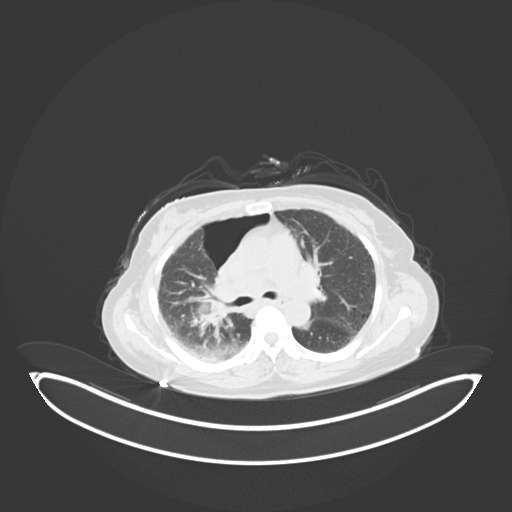
Chest CT, one axial slice; position 35 of 69 along the scan axis; lung window (W 1500 / L -600 HU); 3 mm slice thickness; 512 × 512 image matrix, field of view 500 × 500 mm. Female patient, age 64 years. From the clinical record (not read from this slice): clinical TNM (as recorded): T3 N3 M0.
Outlined on this slice (rectangle marked by the reading radiologist):
- lung tumour (recorded histology: squamous cell carcinoma): bounding box <183,291,245,346> (left, top, right, bottom; pixels)